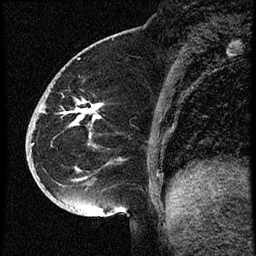
Breast MRI (dynamic contrast-enhanced), one sagittal slice. Position 20 of 60 along the scan axis. Dynamic contrast-enhanced study with each time point stored as its own series, time point 2 of 3 at this slice position (early post-contrast, ordered by acquisition time). 1.5 T. TE 4.2 ms, TR 18.9 ms. 256 × 256 image matrix, field of view 200 × 200 mm. Female patient. Case-level facts recorded for this patient, not image findings: setting: breast cancer imaged before/during neoadjuvant chemotherapy; receptor status: HR-positive, HER2-negative.
Structures marked on this image (semi-automatically segmented with operator editing):
- analysis volume of interest (the breast-tissue region the enhancement analysis was run in; not a lesion): bounding box (x1, y1, x2, y2) in pixels: (30, 87, 114, 173)
- tumour enhancement mask (voxels above the 100 % enhancement threshold inside the analysis volume of interest): (80, 110, 101, 118)